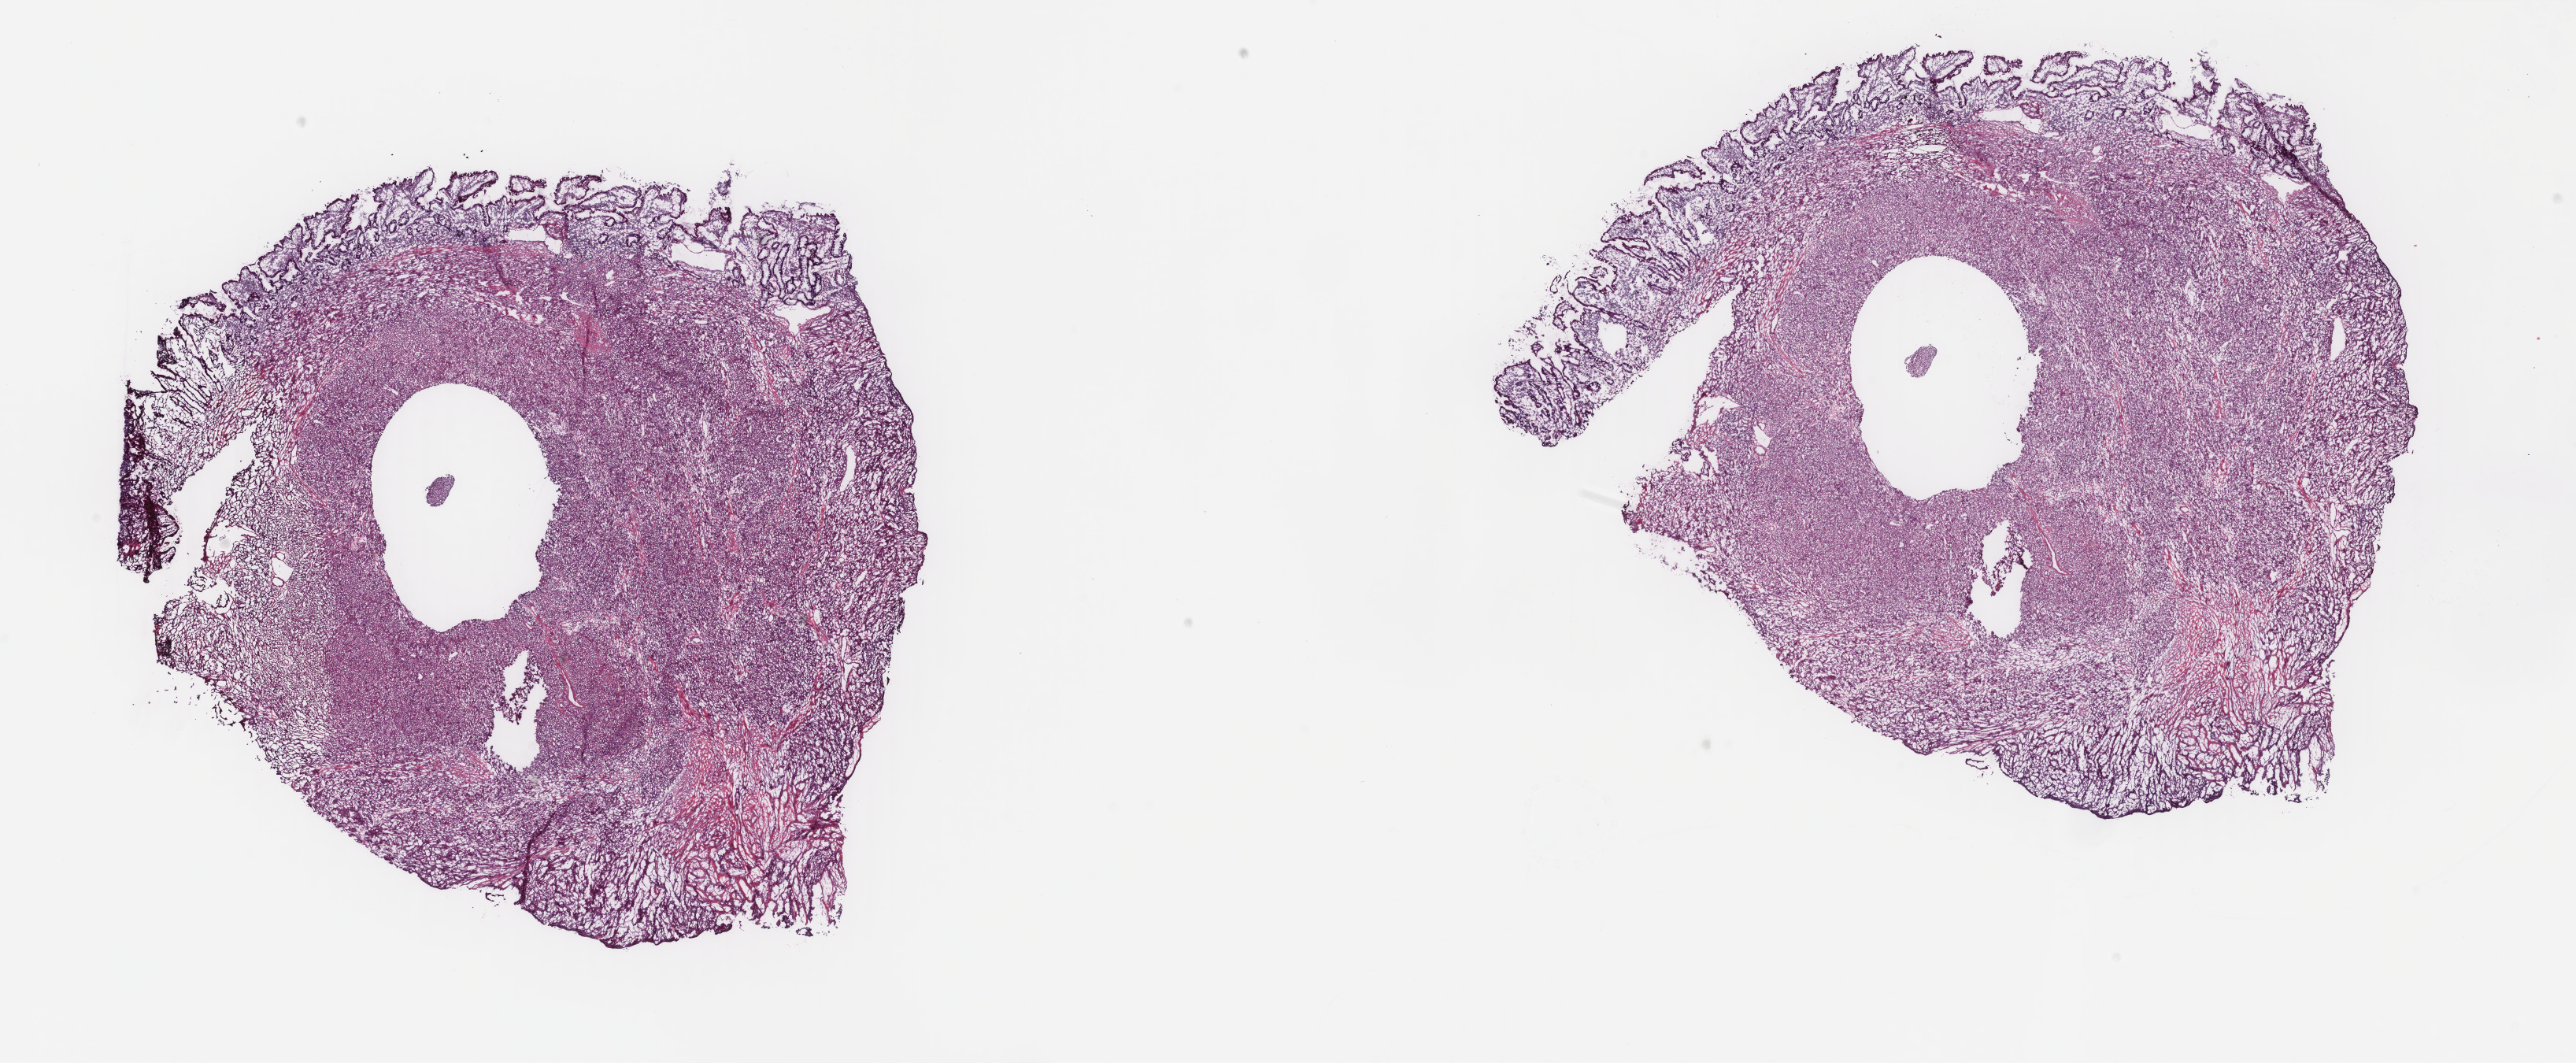
H&E-stained whole-slide image — low-resolution overview of the scanned area, about 26.0 x 10.7 mm (from a 40x scan); frozen section from the top of the tissue portion; sample: primary tumour, retroperitoneum and peritoneum. Male patient; age at initial diagnosis 54 years. Slide review estimates, as recorded: tumour cells 90%, tumour nuclei 90%, normal cells 10%, stromal cells 0%, necrosis 0%. Infiltration values recorded for this section: lymphocyte infiltration 0%, monocyte infiltration 0%, neutrophil infiltration 0%.
Pathologic diagnosis: Leiomyosarcoma, NOS.